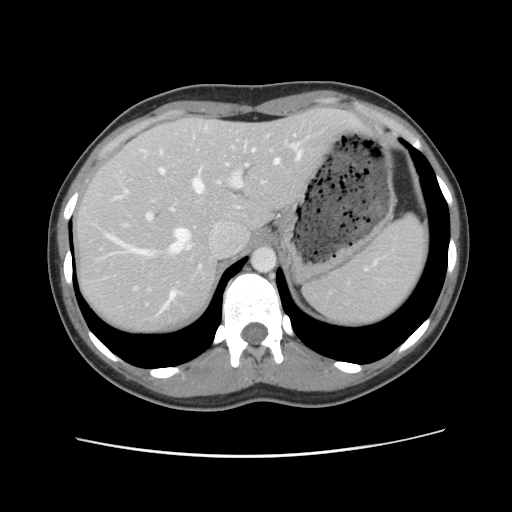
Contrast-enhanced abdominal CT, one axial slice; position 86 of 134 along the scan axis; 120 kVp; intravenous contrast given; soft-tissue window (W 400 / L 40 HU); 2.5 mm slice thickness; 512 × 512 image matrix, field of view 339 × 339 mm. Female patient, age 33 years. From the clinical record (not read from this slice): diagnosis: colorectal cancer liver metastases, imaged before liver resection; multiple liver metastases: yes.
Structures marked on this image (manually delineated by an expert):
- hepatic veins: bounding box [x1, y1, x2, y2] px = [106, 145, 303, 311]
- liver: [75, 109, 359, 335]
- planned liver remnant (the part of the liver to remain after resection): [75, 109, 359, 335]
- portal vein (with intrahepatic branches): [145, 139, 295, 222]
- liver metastasis: [99, 171, 108, 180]